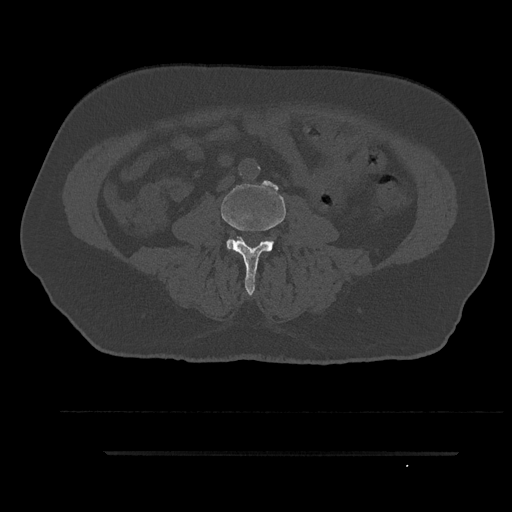
CT including the spine, one axial slice. 120 kVp. Bone window (W 1800 / L 400 HU). 512 × 512 image matrix, field of view 432 × 432 mm. Male patient, age 63 years. Case-level facts recorded for this patient, not image findings: primary cancer: renal; vertebrae with lytic lesions (as recorded): T8.
Annotated regions visible in this slice (semi-automatically segmented with operator editing):
- L3 vertebra: bounding box <221,185,286,296> (left, top, right, bottom; pixels)
- L4 vertebra: <269,241,274,248>